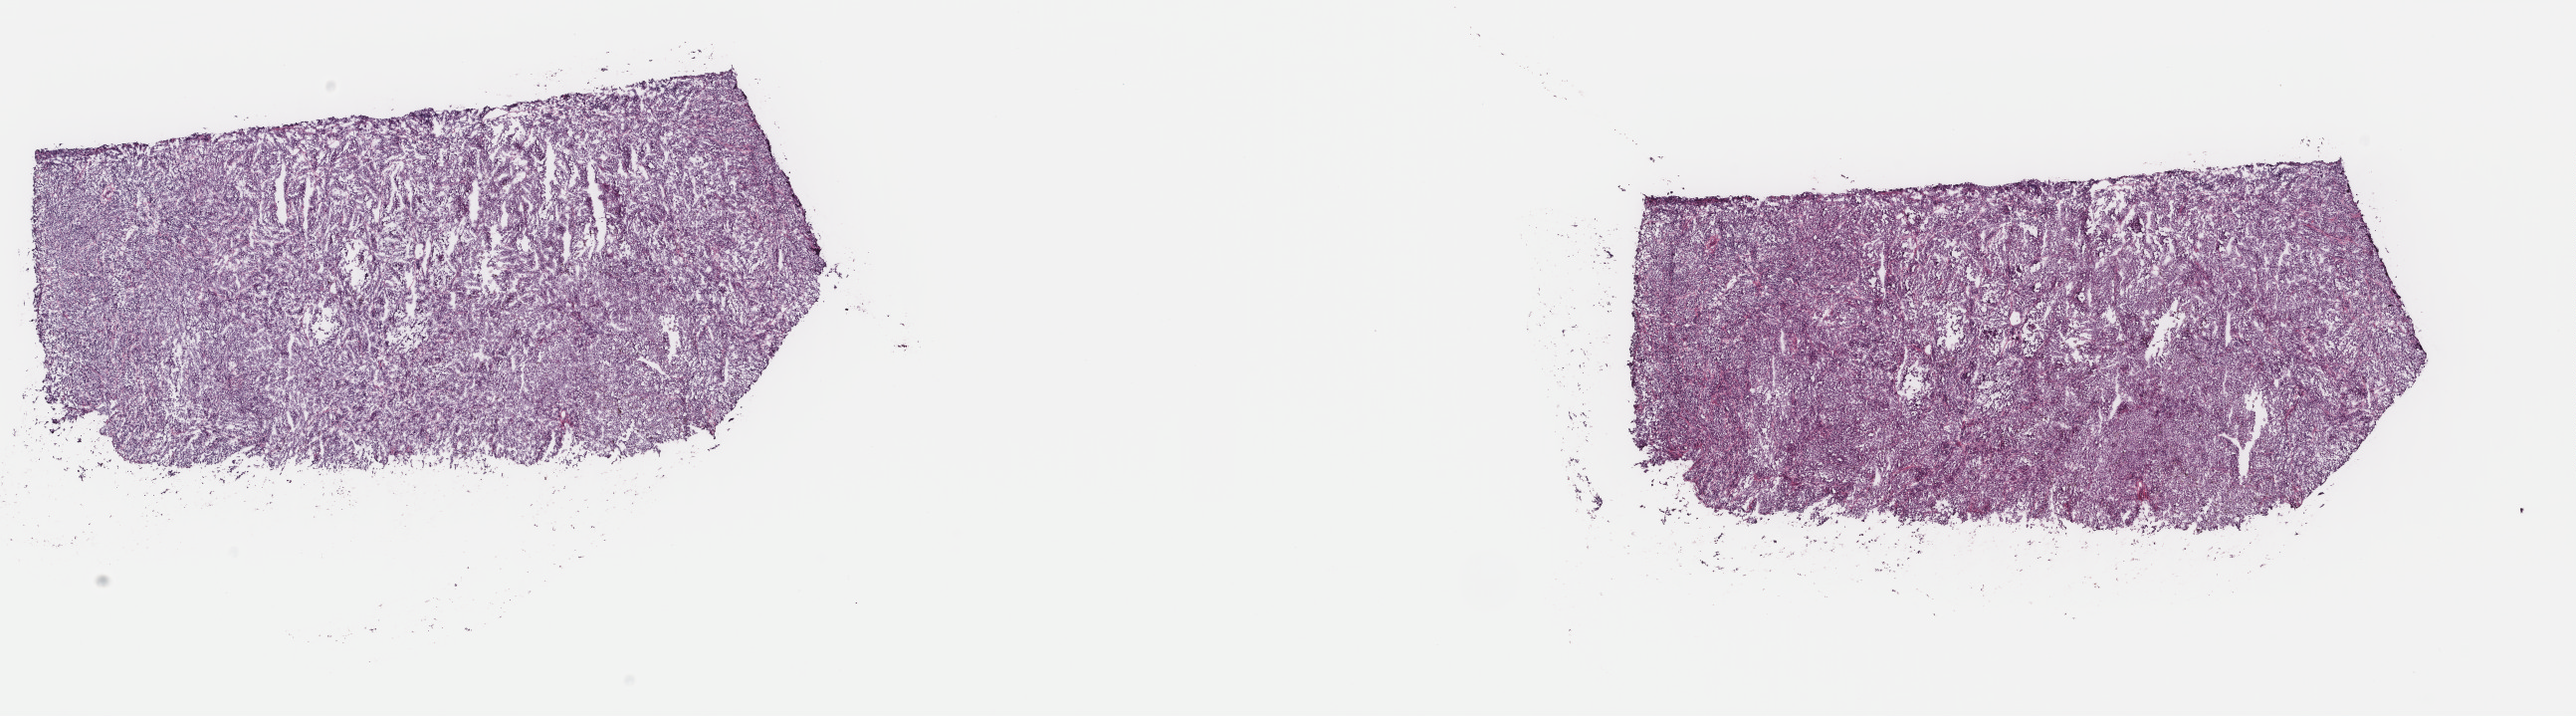
Whole-slide histology image, H&E-stained, a low-resolution overview of the entire scanned area, about 20.5 x 5.7 mm, frozen section, metastatic tumour sample, sampled site: lymph nodes of axilla or arm. Patient: male, age at initial diagnosis 39 years. Pathologist review of this section (percent, as recorded): tumour cells 90%, tumour nuclei 90%, normal cells 0%, stromal cells 10%, necrosis 0%. Infiltration values recorded for this section: lymphocyte infiltration 3%, monocyte infiltration 0%, neutrophil infiltration 0%.
- this section: metastatic tumour tissue
- patient diagnosis: Malignant melanoma, NOS